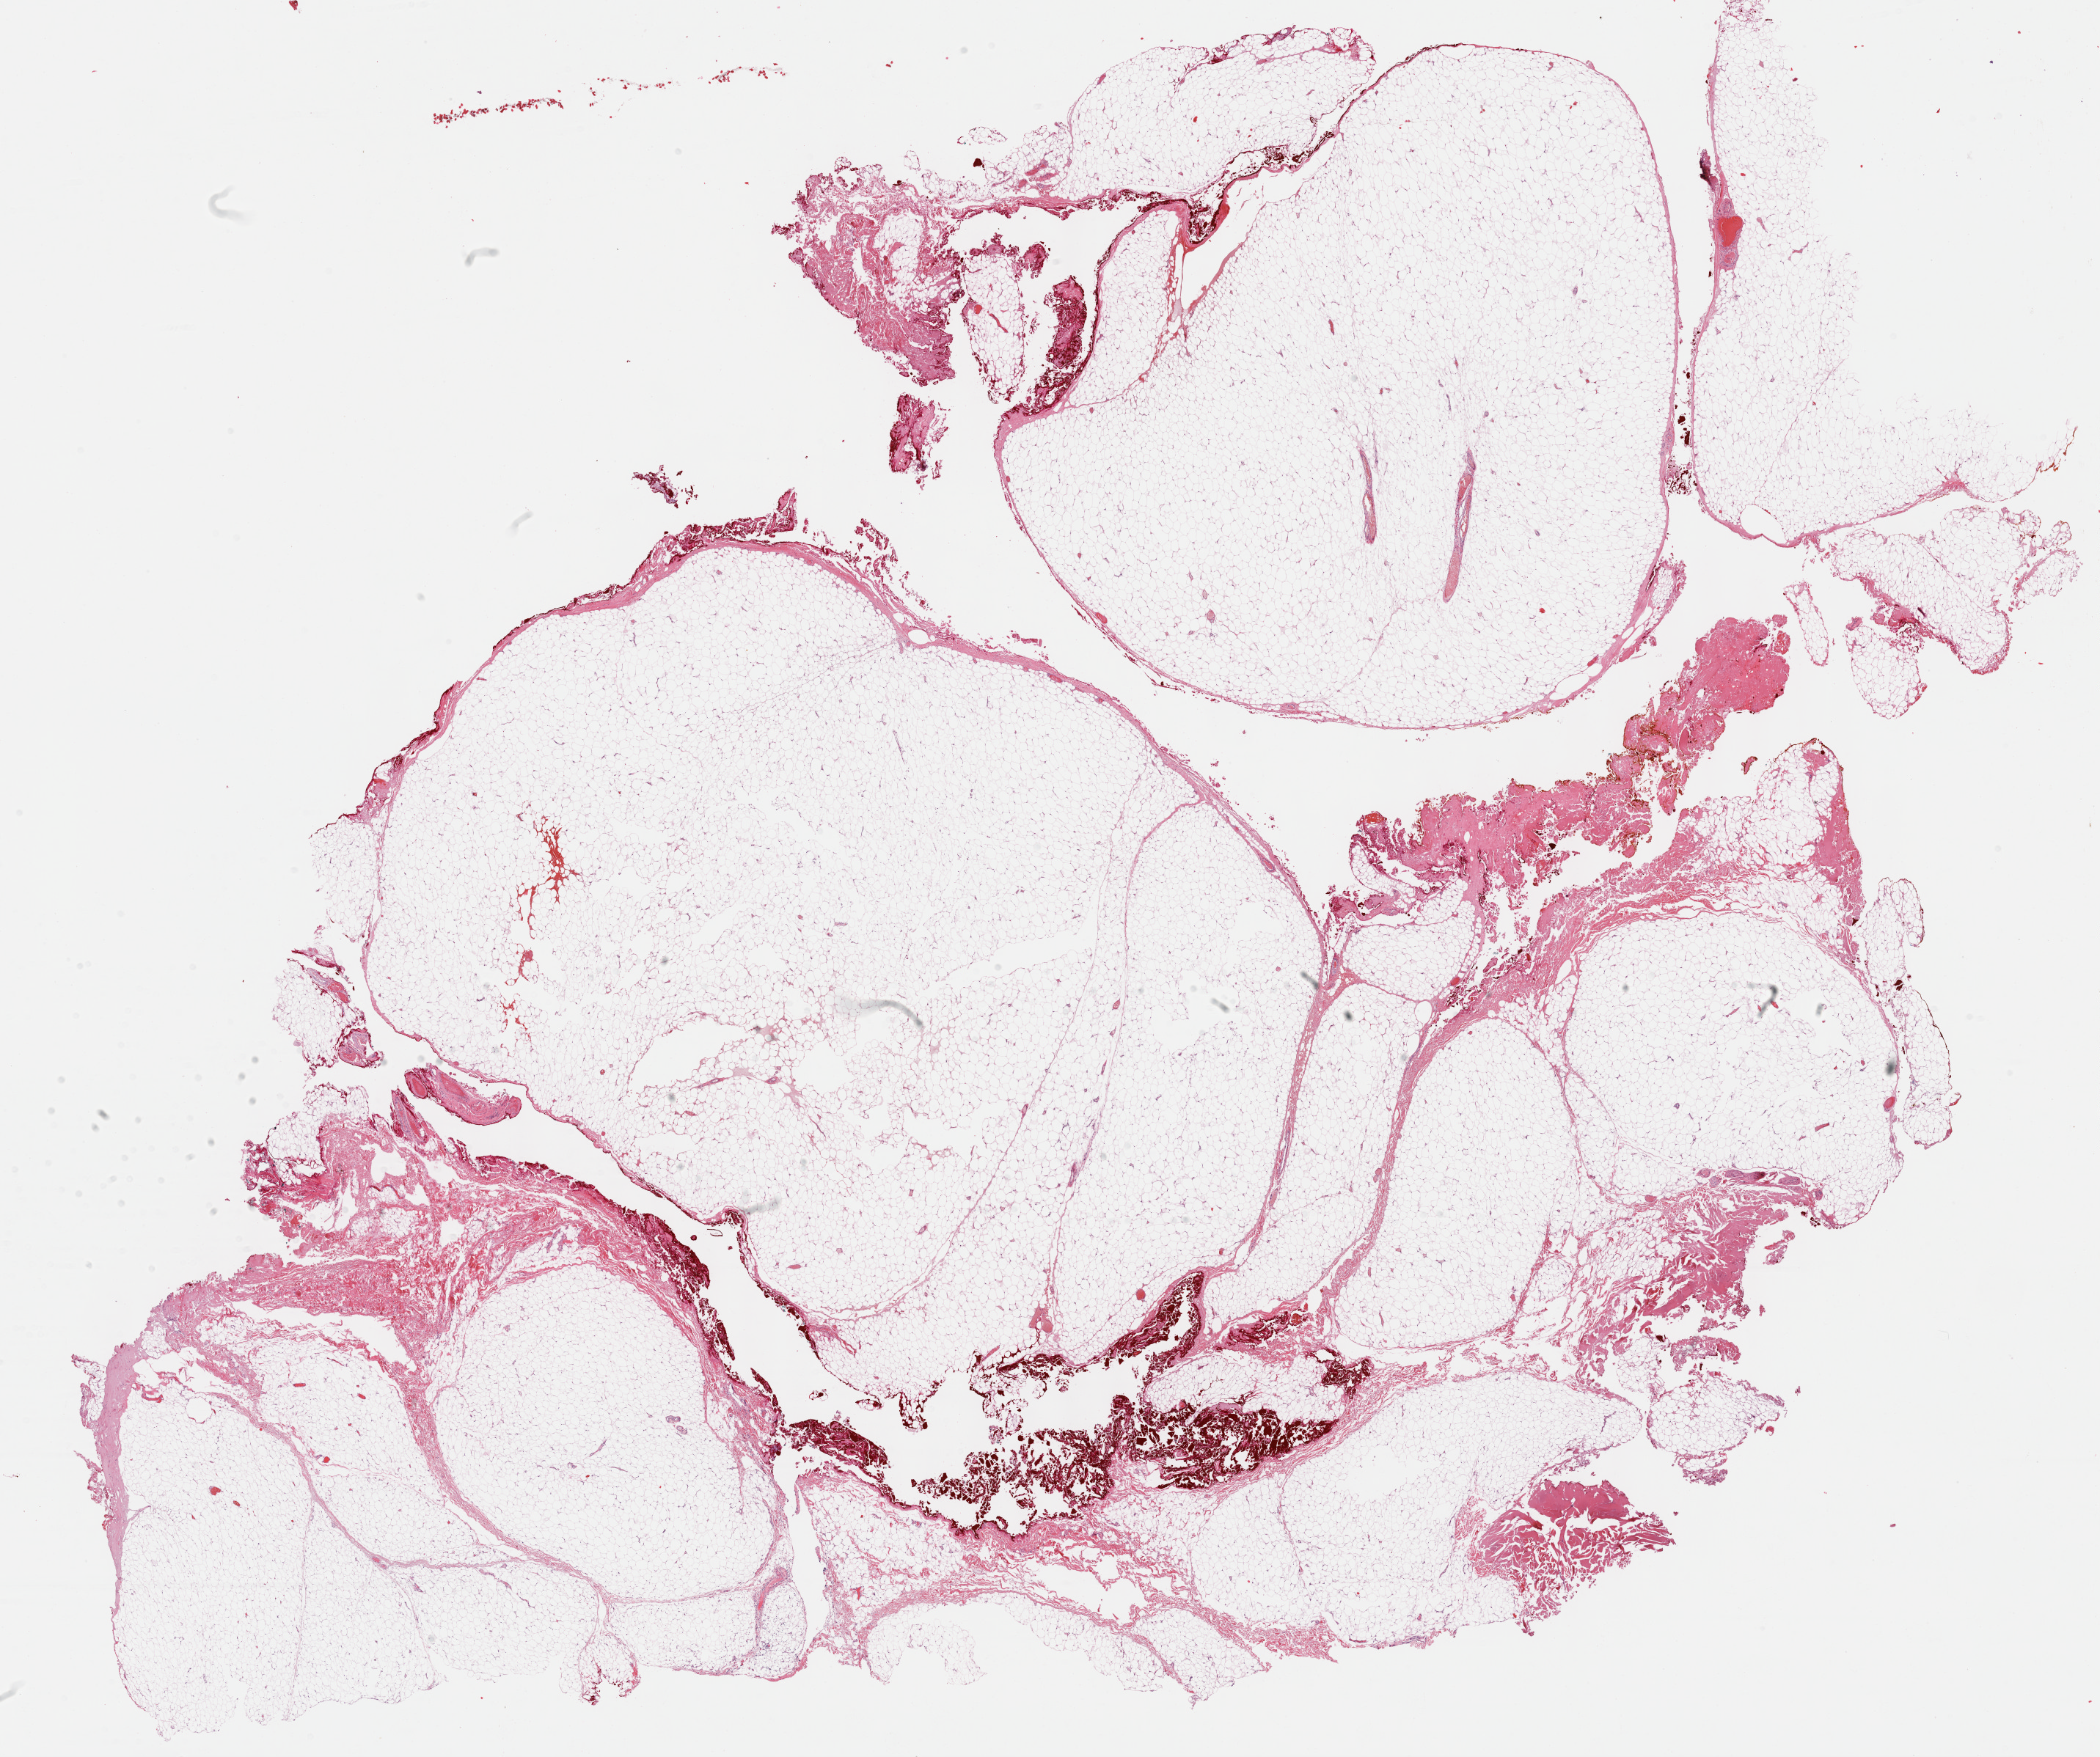
H&E-stained whole-slide image, shown as a low-resolution overview of the whole scanned area (about 23.2 x 19.4 mm, slide scanned at 40x). FFPE section. Connective, subcutaneous and other soft tissues, primary tumour sample. Male patient; age at initial diagnosis 35 years.
* histologic diagnosis: Fibromyxosarcoma (connective, subcutaneous and other soft tissues of lower limb and hip)